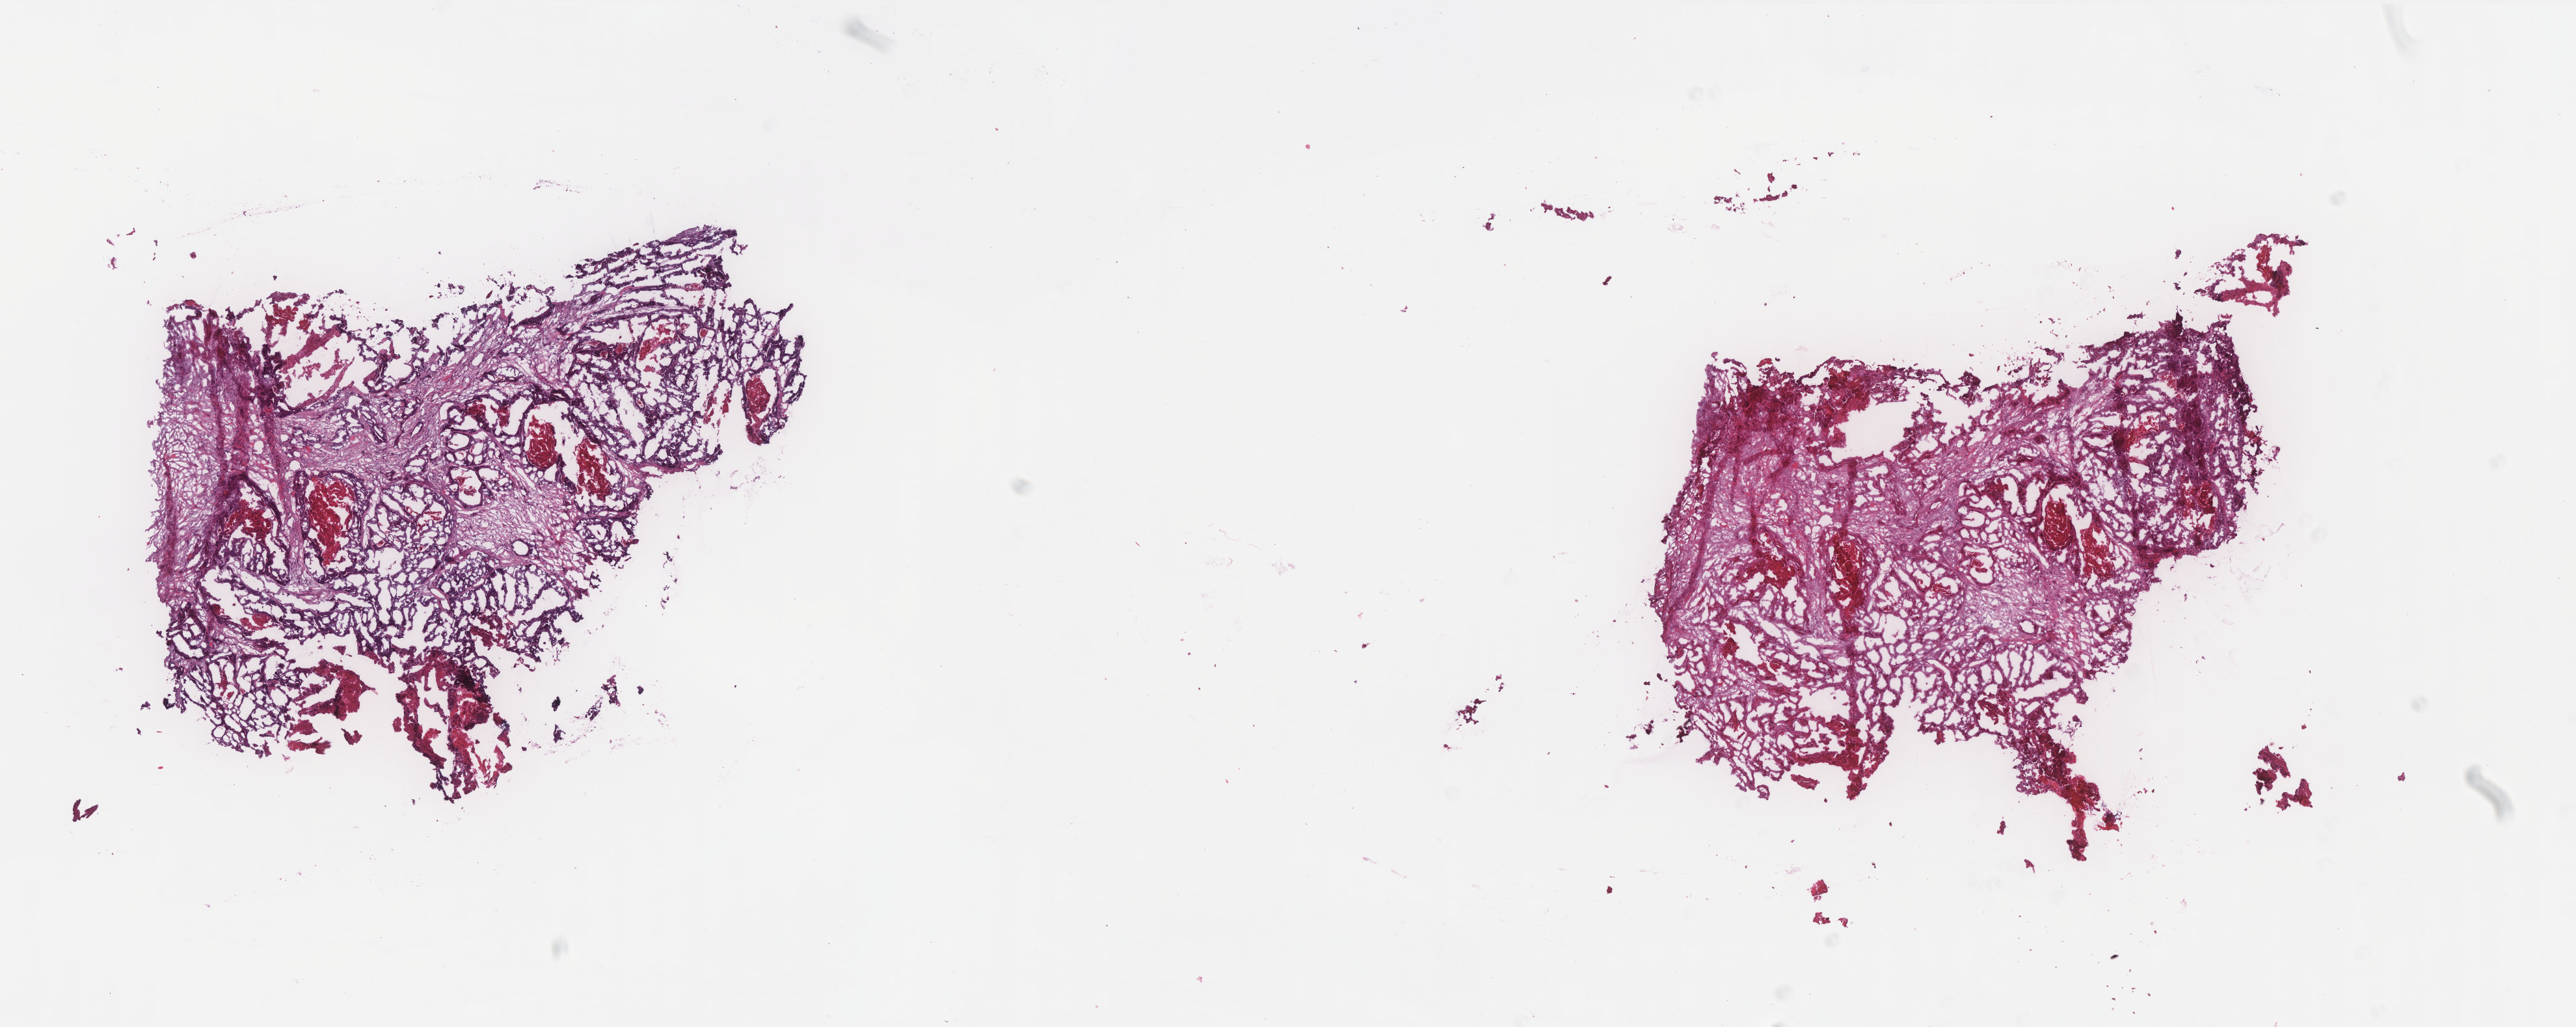
Digitized H&E-stained tissue section (whole slide) — low-resolution overview of the scanned area, about 15.9 x 6.3 mm (from a 40x scan); frozen section from the top of the tissue portion; sample: primary tumour, colon. Female patient; age at initial diagnosis 79 years. Slide review estimates, as recorded: tumour cells 80%, tumour nuclei 70%, normal cells 0%, stromal cells 10%, necrosis 10%. Inflammatory infiltration, as recorded: lymphocyte infiltration 0%, monocyte infiltration 0%, neutrophil infiltration 0%.
Histologic diagnosis: Adenocarcinoma, NOS (sigmoid colon). AJCC pathologic stage: IIA.